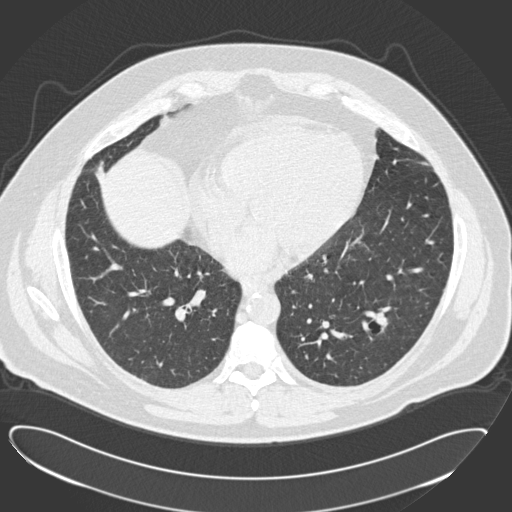
Chest CT (low-dose screening protocol), one axial image, baseline annual screen, lung window (W 1500 / L -600 HU), standard (soft-tissue) reconstruction kernel (B30f), slice 90 of 183 in the series, 512 × 512 image matrix, field of view 426 × 426 mm. Male, age 57 years at enrolment. Current smoker at enrolment.
- Expert reader's lesion annotation, bounding box <354,299,407,349> (left, top, right, bottom; pixels).
- The screening reader recorded 2 non-calcified nodules or masses ≥4 mm on this exam (left lower lobe, left lower lobe); which of them this box marks is not recorded.
- Participant outcome: lung cancer diagnosed 791 days after this screen (after the third annual screen) — squamous cell carcinoma, NOS, left lower lobe, moderately differentiated (G2), stage IA (AJCC 6th edition), 22 mm at pathology.